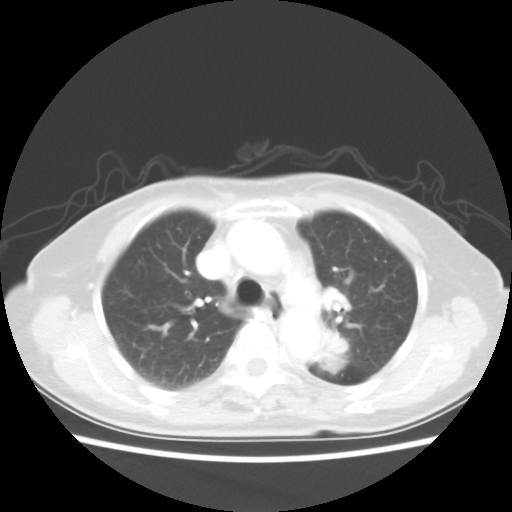
Chest CT, one axial slice; position 34 of 50 along the scan axis; lung window (W 1500 / L -600 HU); 5 mm slice thickness; 512 × 512 image matrix, field of view 335 × 335 mm. Patient: female, 81 years. From the clinical record (not read from this slice): clinical TNM (as recorded): T2 N0 M1a.
Structures marked on this image (rectangle marked by the reading radiologist):
- lung tumour (recorded histology: squamous cell carcinoma): bounding box [x1, y1, x2, y2] px = [314, 323, 348, 371]